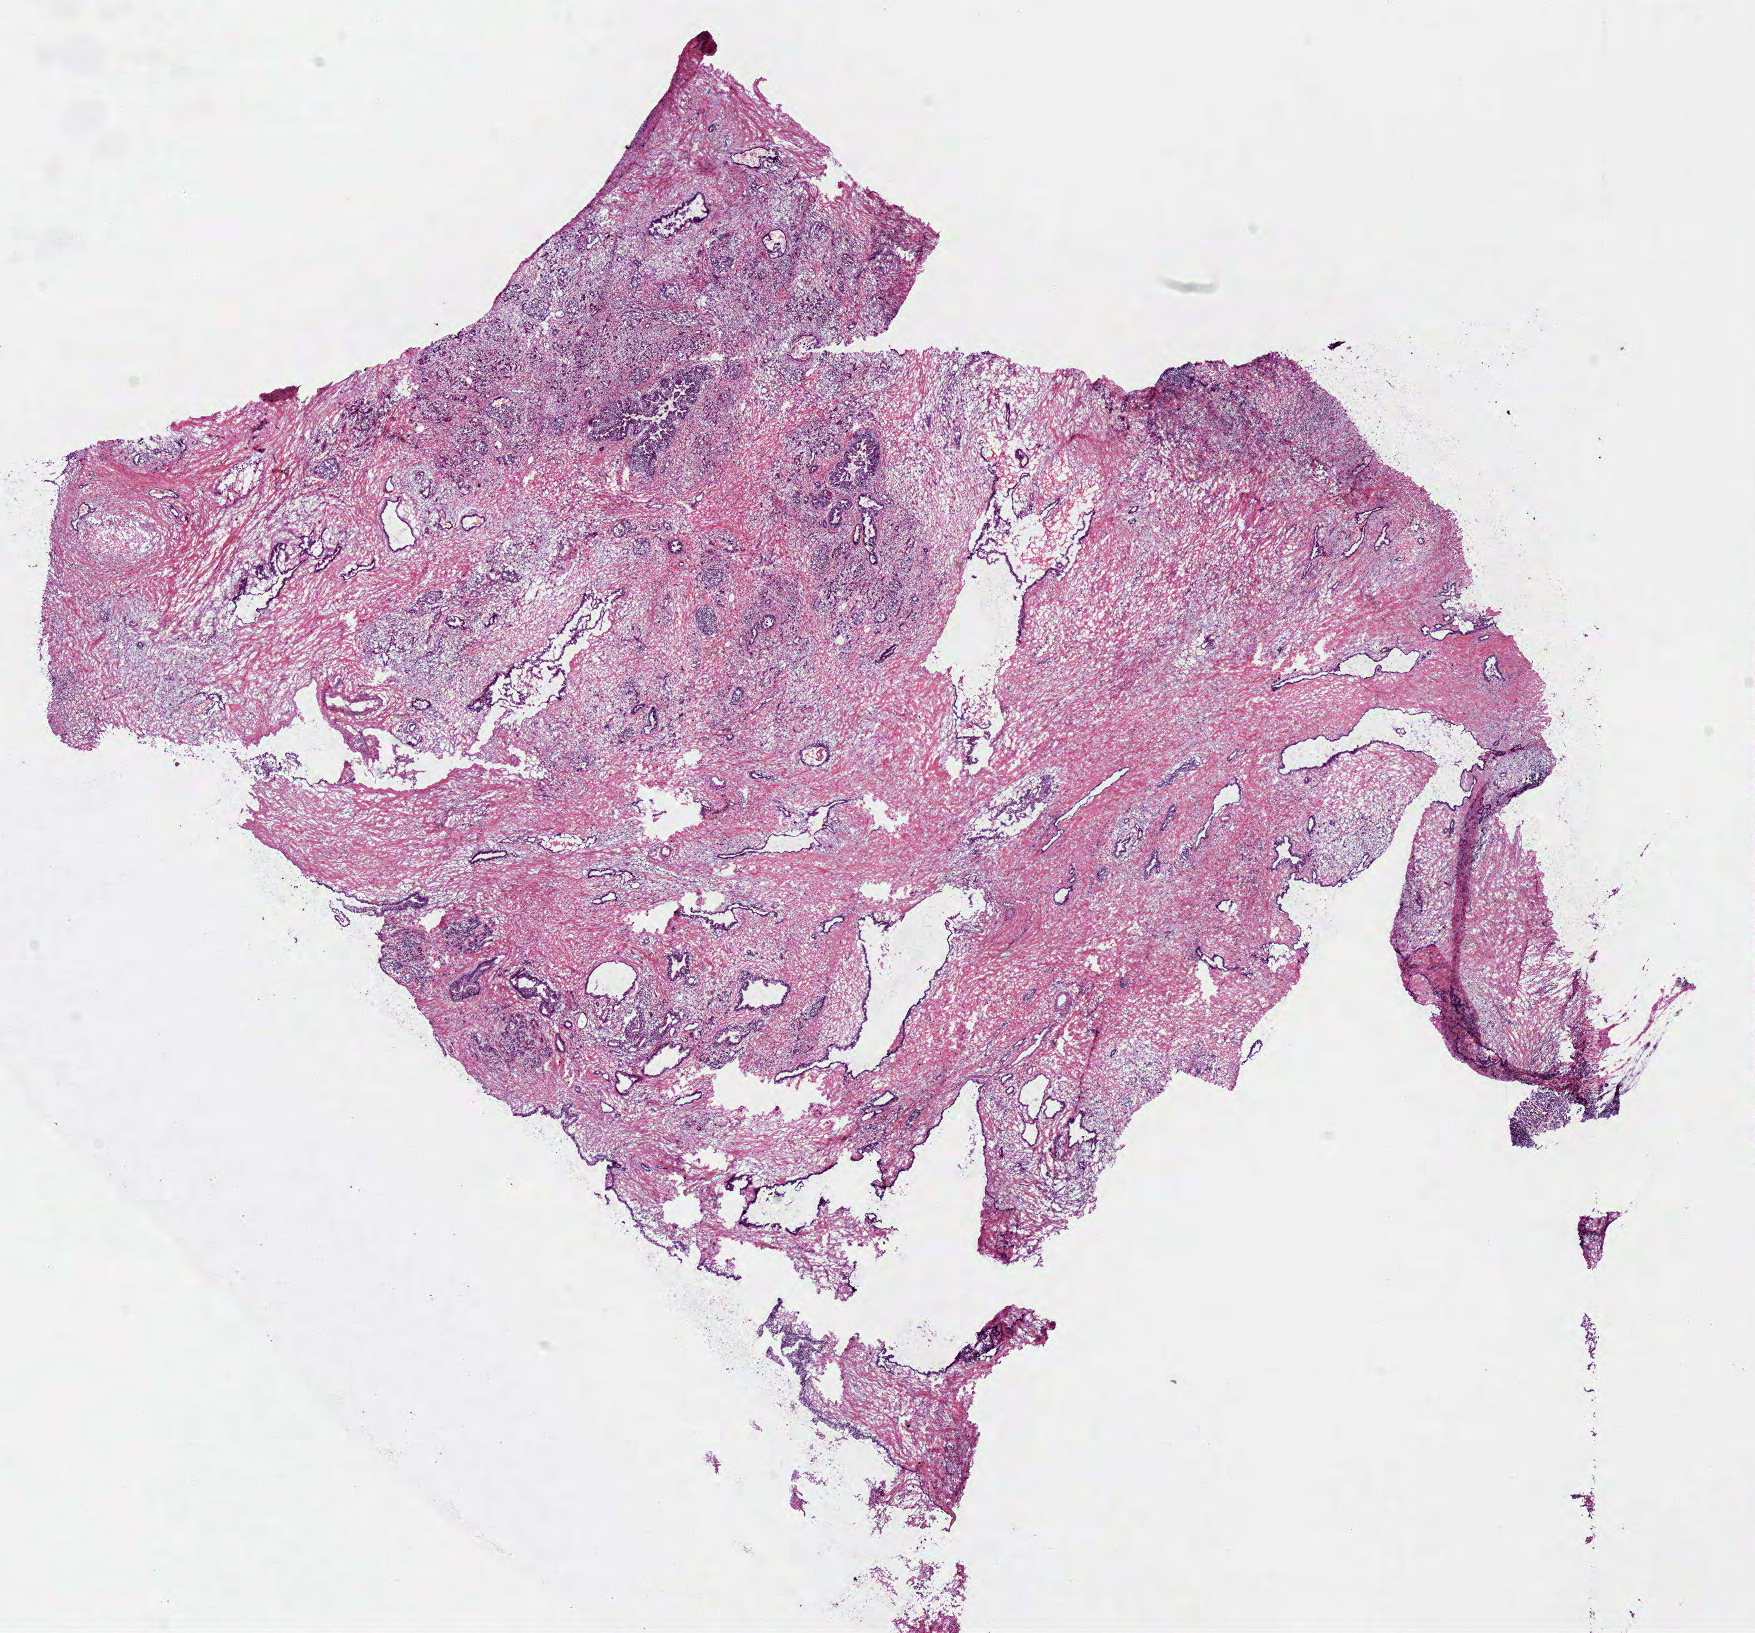
Digitized H&E tissue section (whole slide), low-resolution overview of the scanned area, about 13.8 x 12.9 mm (from a 40x scan). Frozen section. Pancreas, primary tumour sample. Male patient; age at initial diagnosis 71 years. Histologic grade: G1 (well differentiated). Pathologist review of this section (percent, as recorded): tumour cells 70%, tumour nuclei 70%, normal cells 0%, stromal cells 30%, necrosis 0%.
Lymph nodes positive (case pathology): 1 of 13 examined. Histologic diagnosis: Infiltrating duct carcinoma, NOS (head of pancreas). AJCC pathologic stage: IV (6th edition).